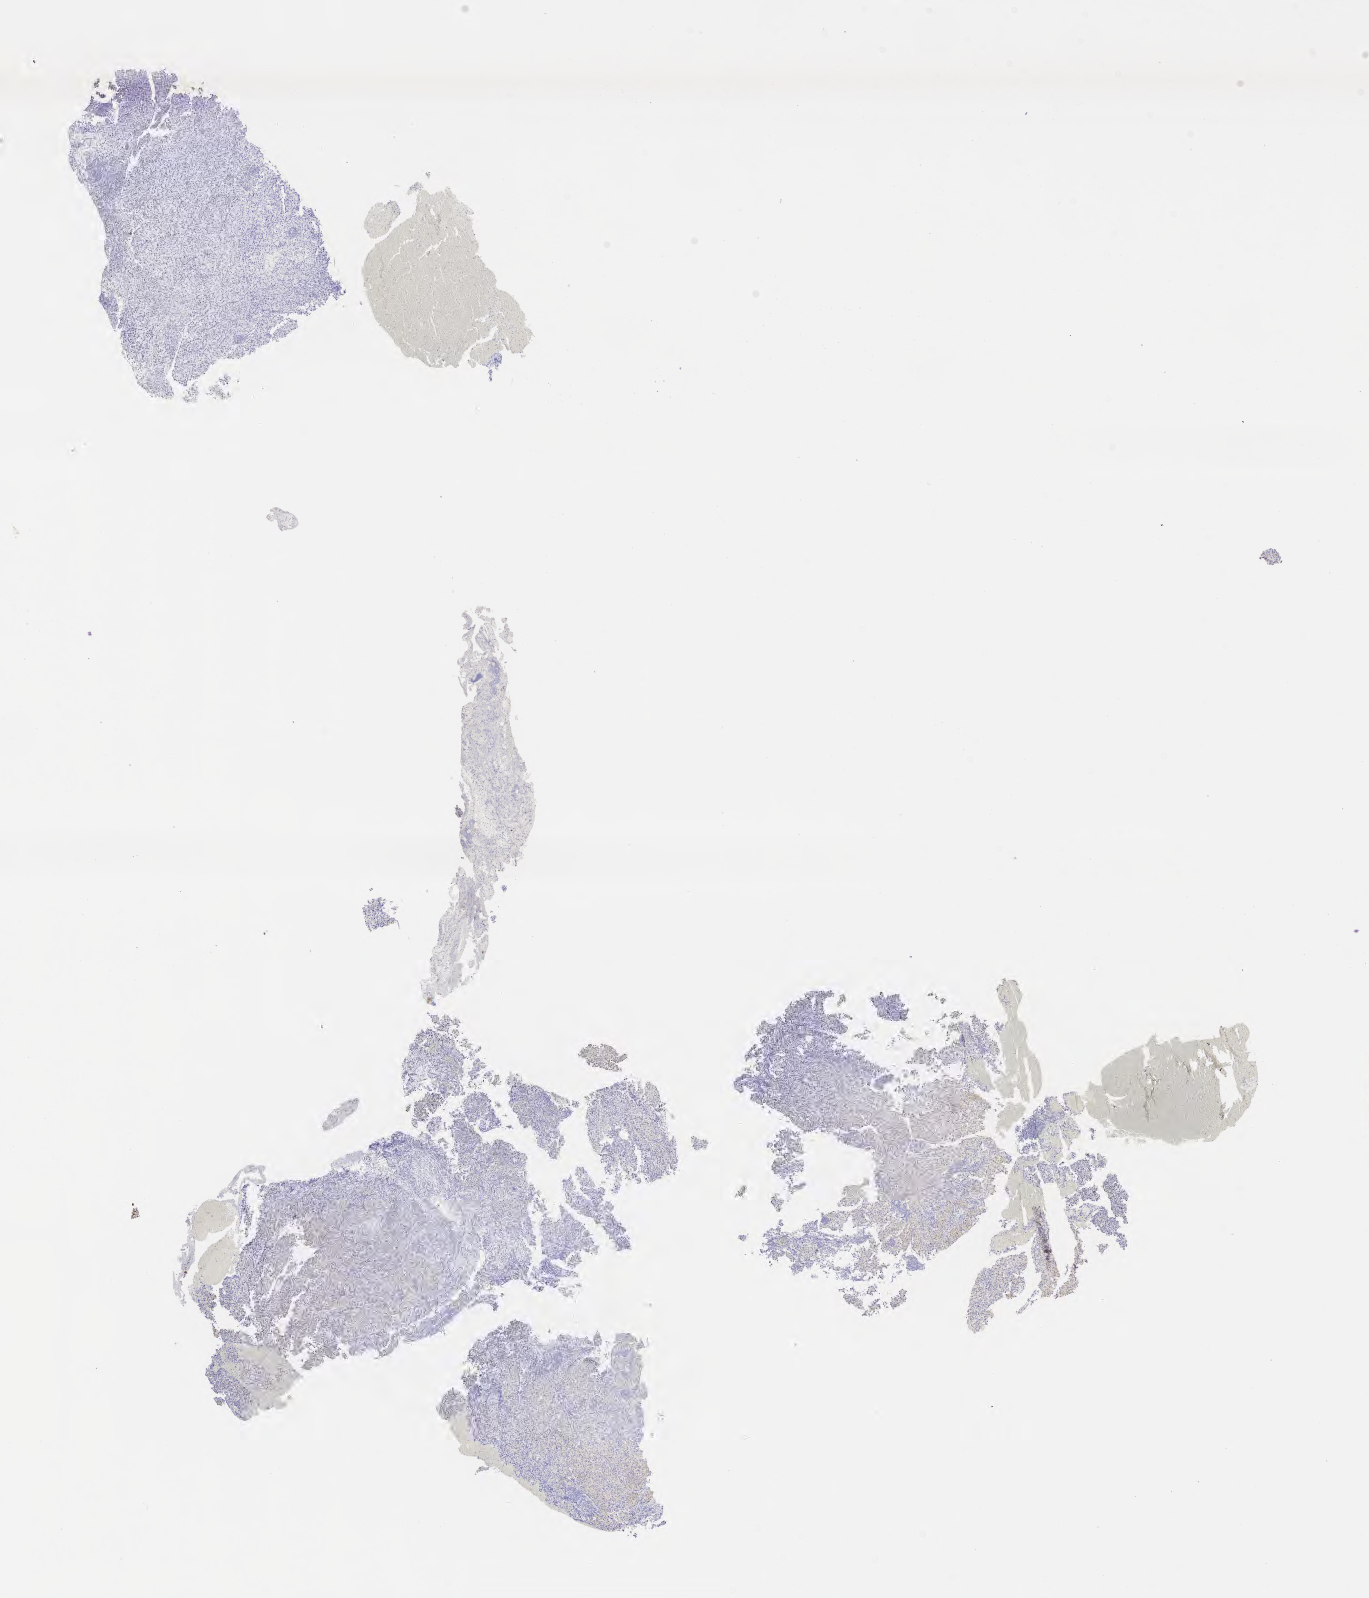
Immunohistochemistry (IHC) whole-slide image stained for p63, shown as a low-resolution overview of the whole scanned area (about 11.1 x 12.9 mm). Tumor tissue. Anatomic site: cervix. Patient: female, aged 33.
Histologic diagnosis: Squamous cell carcinoma, large cell, nonkeratinizing, NOS.